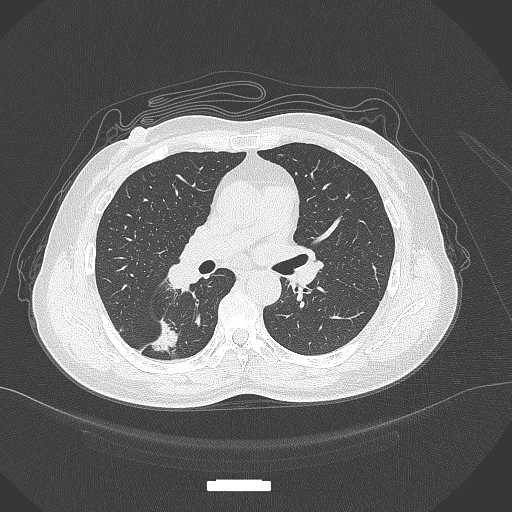
Chest CT, one axial slice; slice 171 of 352 in the series (ordered by position); reconstruction kernel B70f; 120 kVp; lung window (W 1500 / L -600 HU); 512 × 512 image matrix, field of view 400 × 400 mm. Female patient, age 55 years. From the clinical record (not read from this slice): clinical TNM (as recorded): T1c N1 M0.
Structures marked on this image (bounding box drawn by a radiologist):
- lung tumour (recorded histology: adenocarcinoma): bounding box <148,311,183,353> (left, top, right, bottom; pixels)